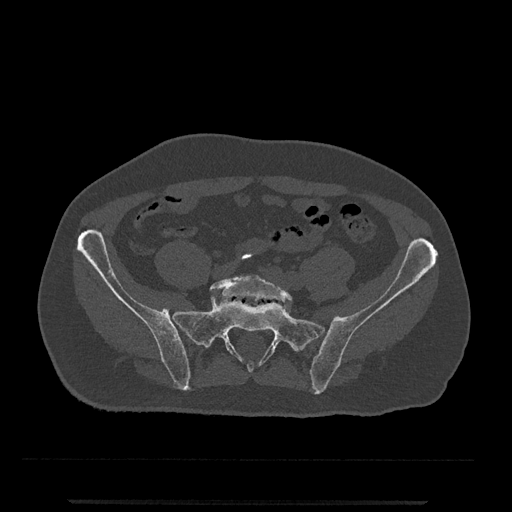
CT including the spine, one axial slice. Slice 27 of 797 in the series (ordered by position). Reconstruction kernel Br40s/3. 120 kVp. Bone window (W 1800 / L 400 HU). 512 × 512 image matrix, field of view 419 × 419 mm. Male patient, age 63 years. From the clinical record (not read from this slice): primary cancer: prostate.
Outlined on this slice (semi-automatic segmentation, software-assisted and operator-edited):
- L5 vertebra: box from (x=210, y=275) to (x=292, y=307) px